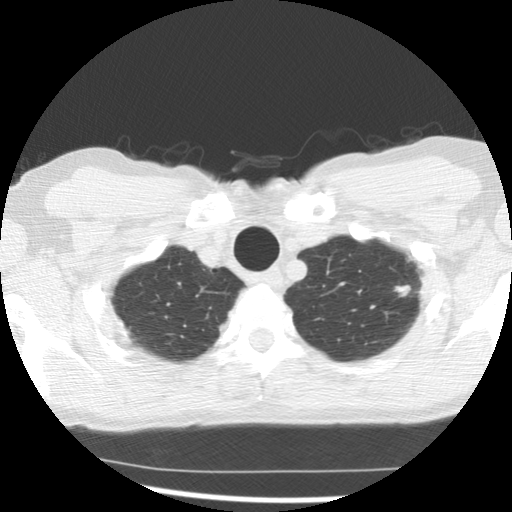
Low-dose screening chest CT, one axial slice. Slice 125 of 145 in the series (ordered by position). Reconstruction kernel STANDARD. 140 kVp. Lung window (W 1500 / L -600 HU). 2.5 mm slice thickness. 512 × 512 image matrix, field of view 320 × 320 mm.
Outlined on this slice (expert manual segmentation):
- lesion 2 (nodule, upper lobe of left lung): bounding box [x1, y1, x2, y2] px = [394, 285, 411, 297]